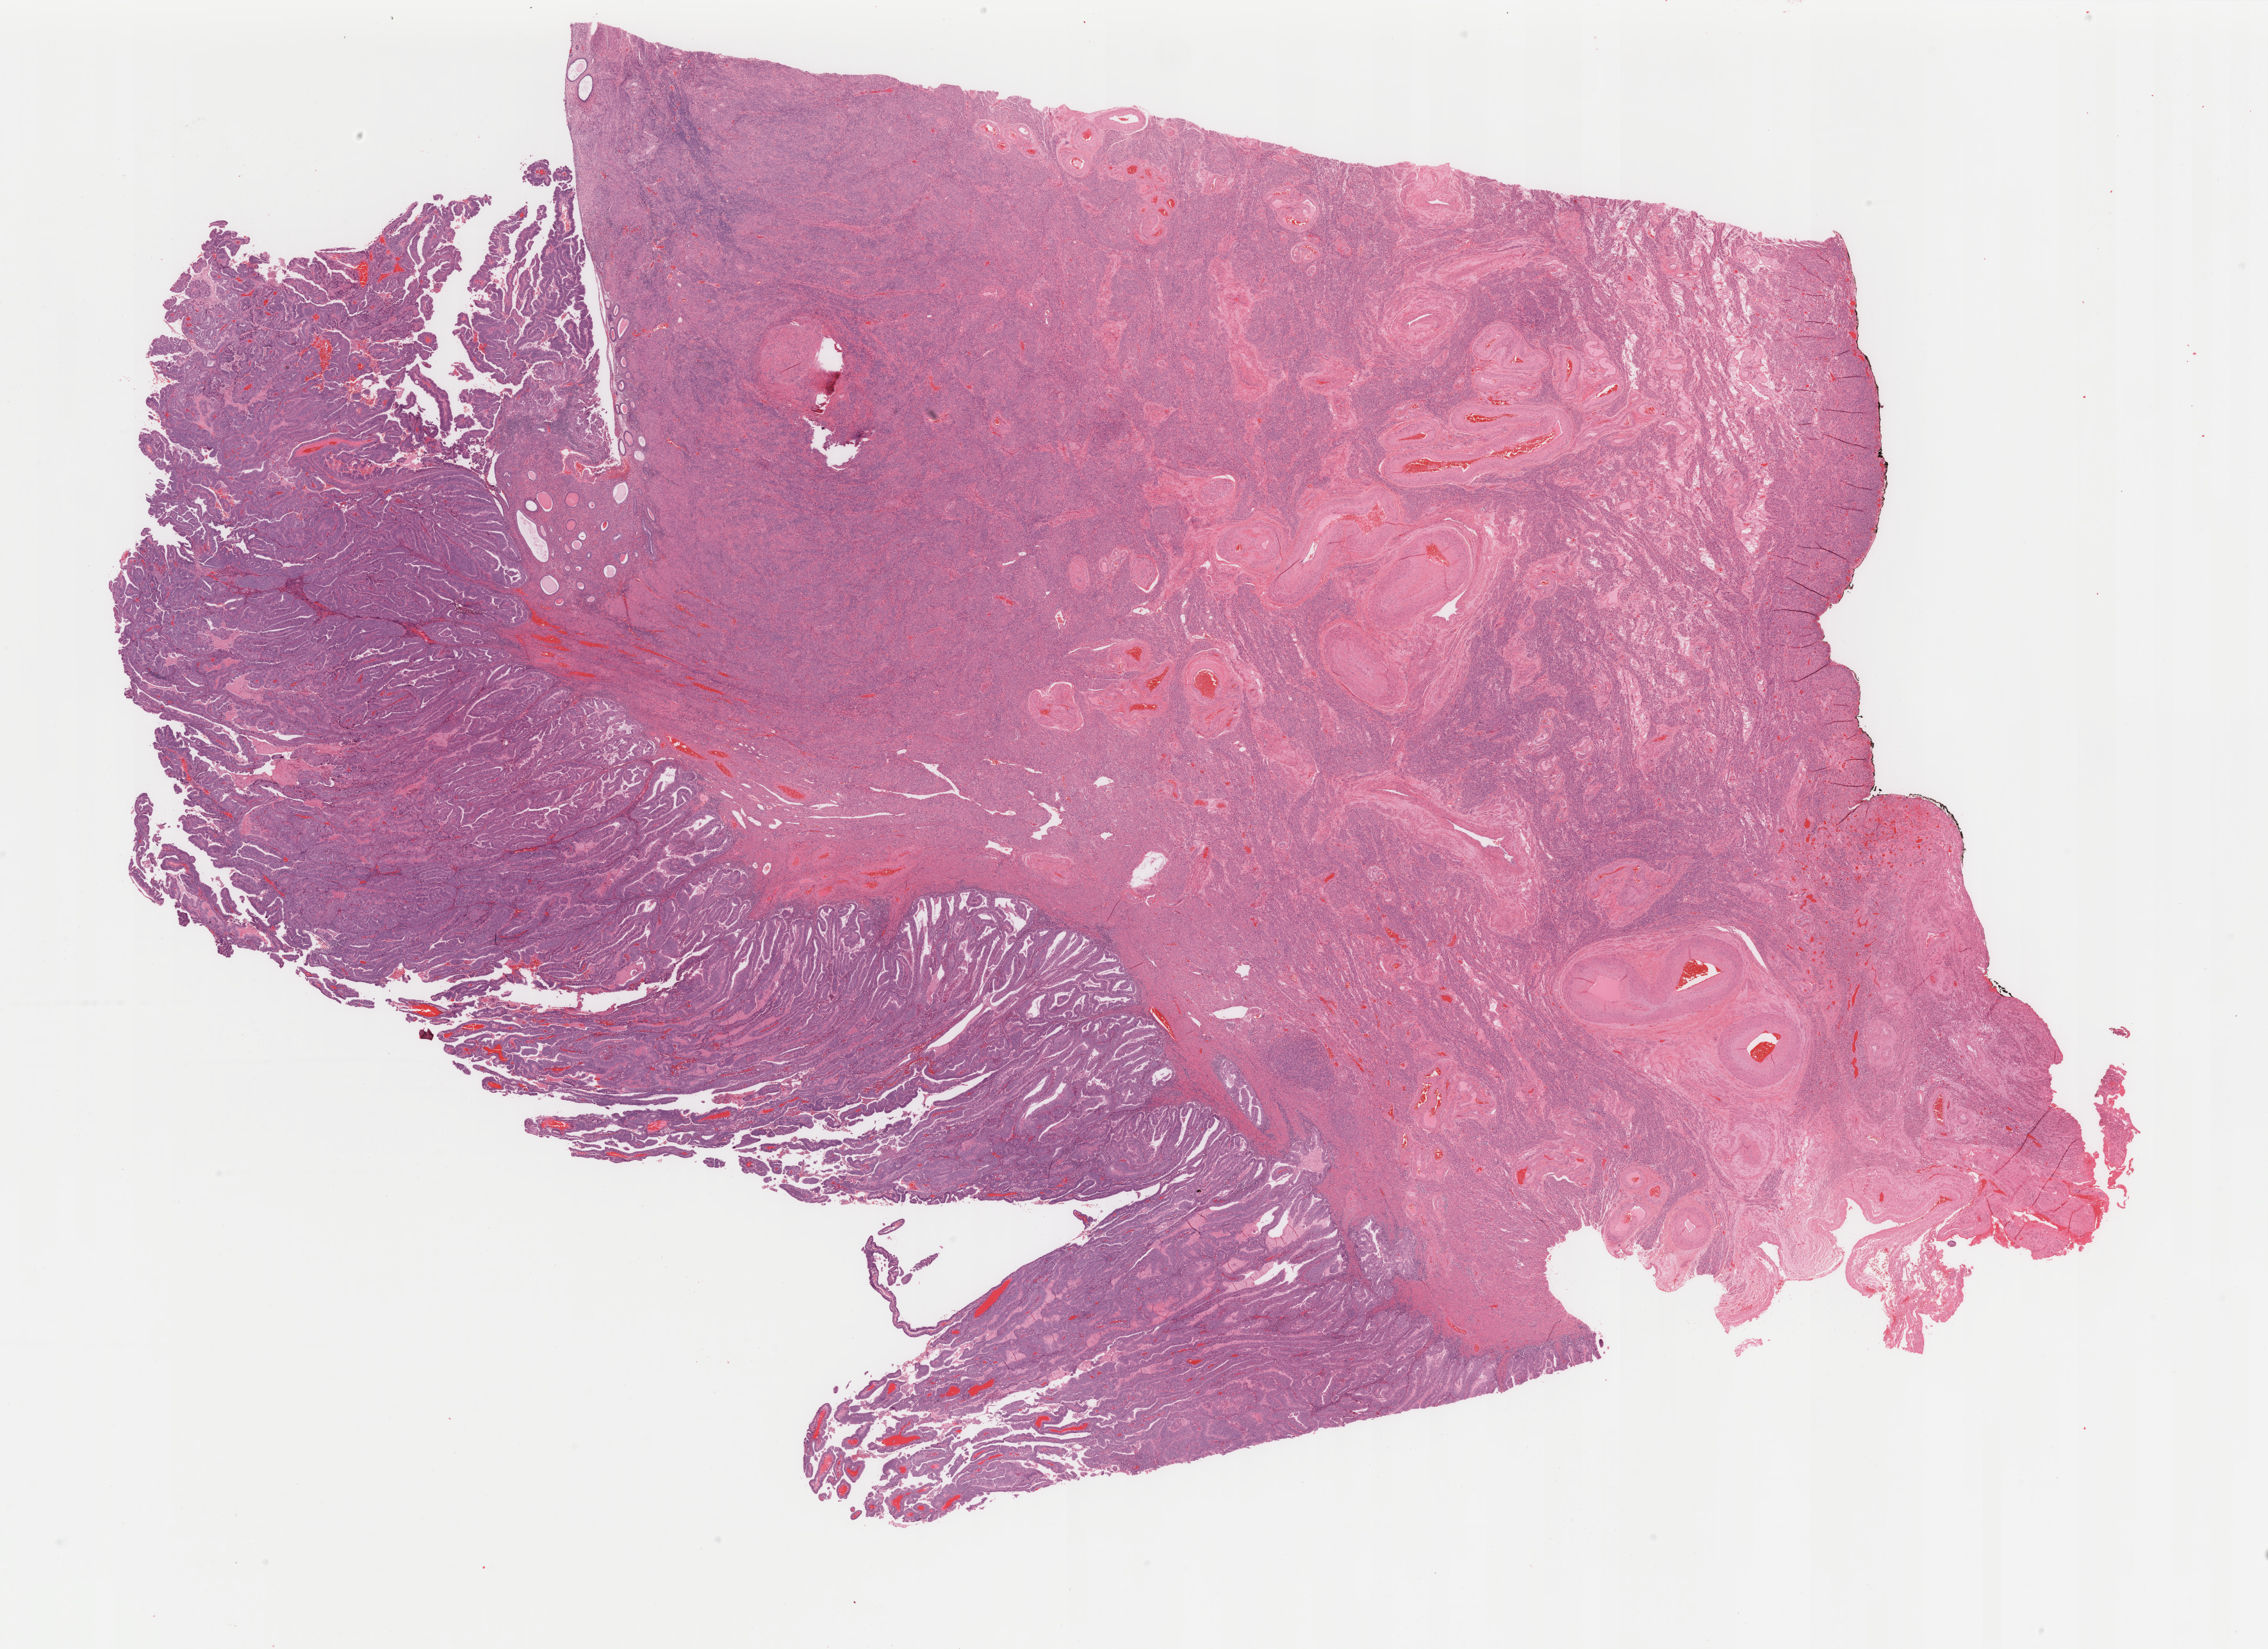
Digitized H&E tissue section (whole slide) — shown as a low-resolution overview of the whole scanned area (about 28.1 x 20.4 mm, slide scanned at 40x); formalin-fixed paraffin-embedded (FFPE) diagnostic section; sample: primary tumour, uterus. Female patient; age at initial diagnosis 73 years. Histologic grade: G2 (moderately differentiated).
FIGO stage: IB. Lymph nodes positive (case pathology): 0 of 17 examined. Pathologic diagnosis: Endometrioid adenocarcinoma, NOS (endometrium).